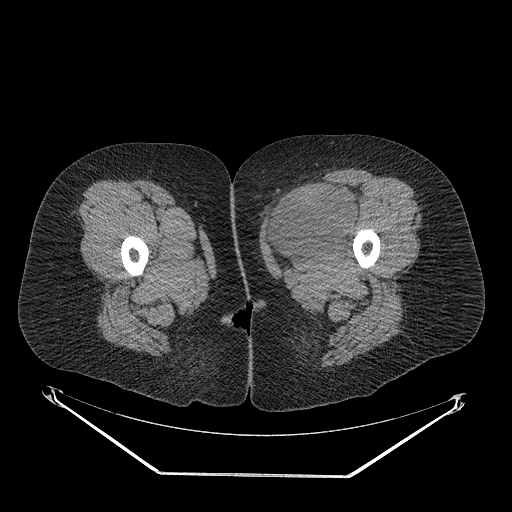
CT of an extremity soft-tissue mass (from a PET/CT study), one axial slice. Slice 28 of 267 in the series (ordered by position). 140 kVp. Soft-tissue window (W 400 / L 40 HU). 3.75 mm slice thickness. 512 × 512 image matrix. Female patient. From the clinical record (not read from this slice): histological type: myxofibrosarcoma; grade: intermediate; site of the primary tumour: left thigh.
Outlined on this slice (expert contour drawn on MRI and transferred to this co-registered scan by the dataset authors):
- gross tumour volume including surrounding oedema: box from (x=265, y=187) to (x=357, y=259) px
- gross tumour volume (mass): (x=267, y=187)–(x=355, y=252)